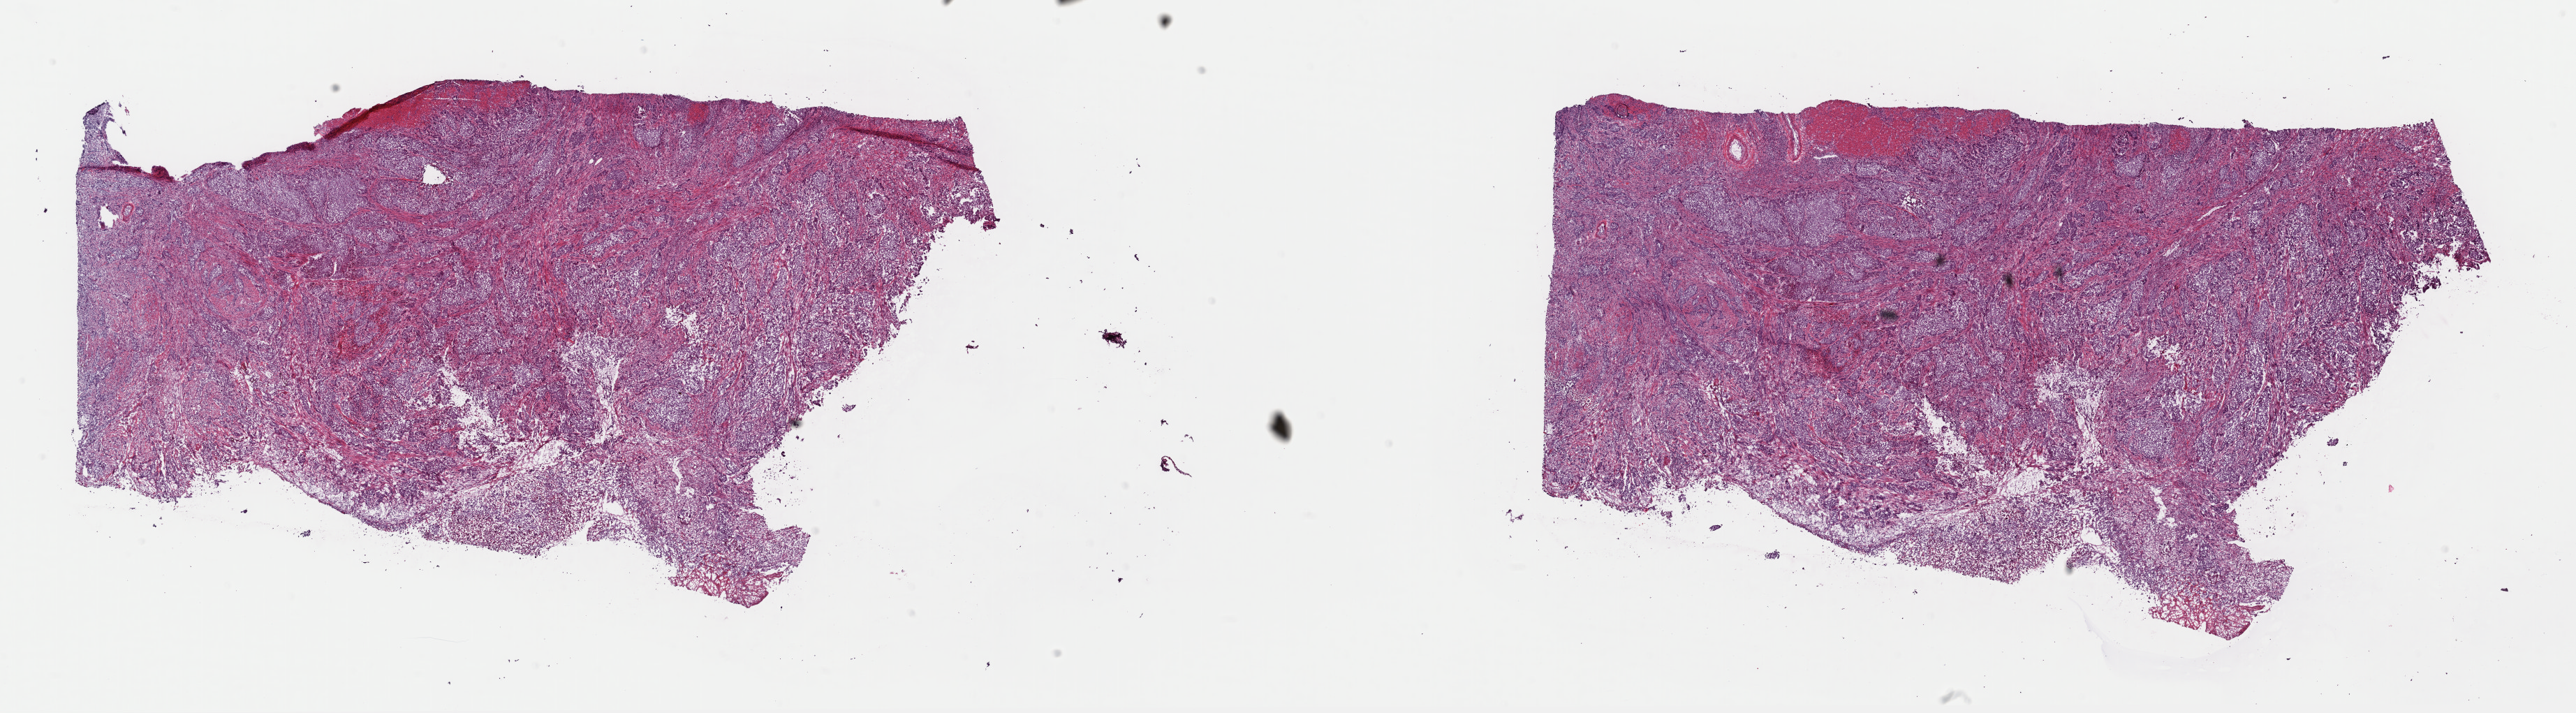
Hematoxylin and eosin (H&E) stained whole-slide image — whole scanned area (about 29.1 x 8.1 mm) shown as a low-resolution overview. Frozen section. Bladder, primary tumour sample. Male, age 68 years at initial diagnosis. Histologic grade: high grade. Pathologist review of this section (percent, as recorded): tumour cells 75%, tumour nuclei 75%, normal cells 0%, stromal cells 25%, necrosis 0%. Infiltration values recorded for this section: lymphocyte infiltration 5%, monocyte infiltration 0%, neutrophil infiltration 0%.
Pathologic diagnosis: Transitional cell carcinoma (lateral wall of bladder). Lymph nodes positive (case pathology): 1 of 17 examined. AJCC pathologic stage: IV (7th edition).